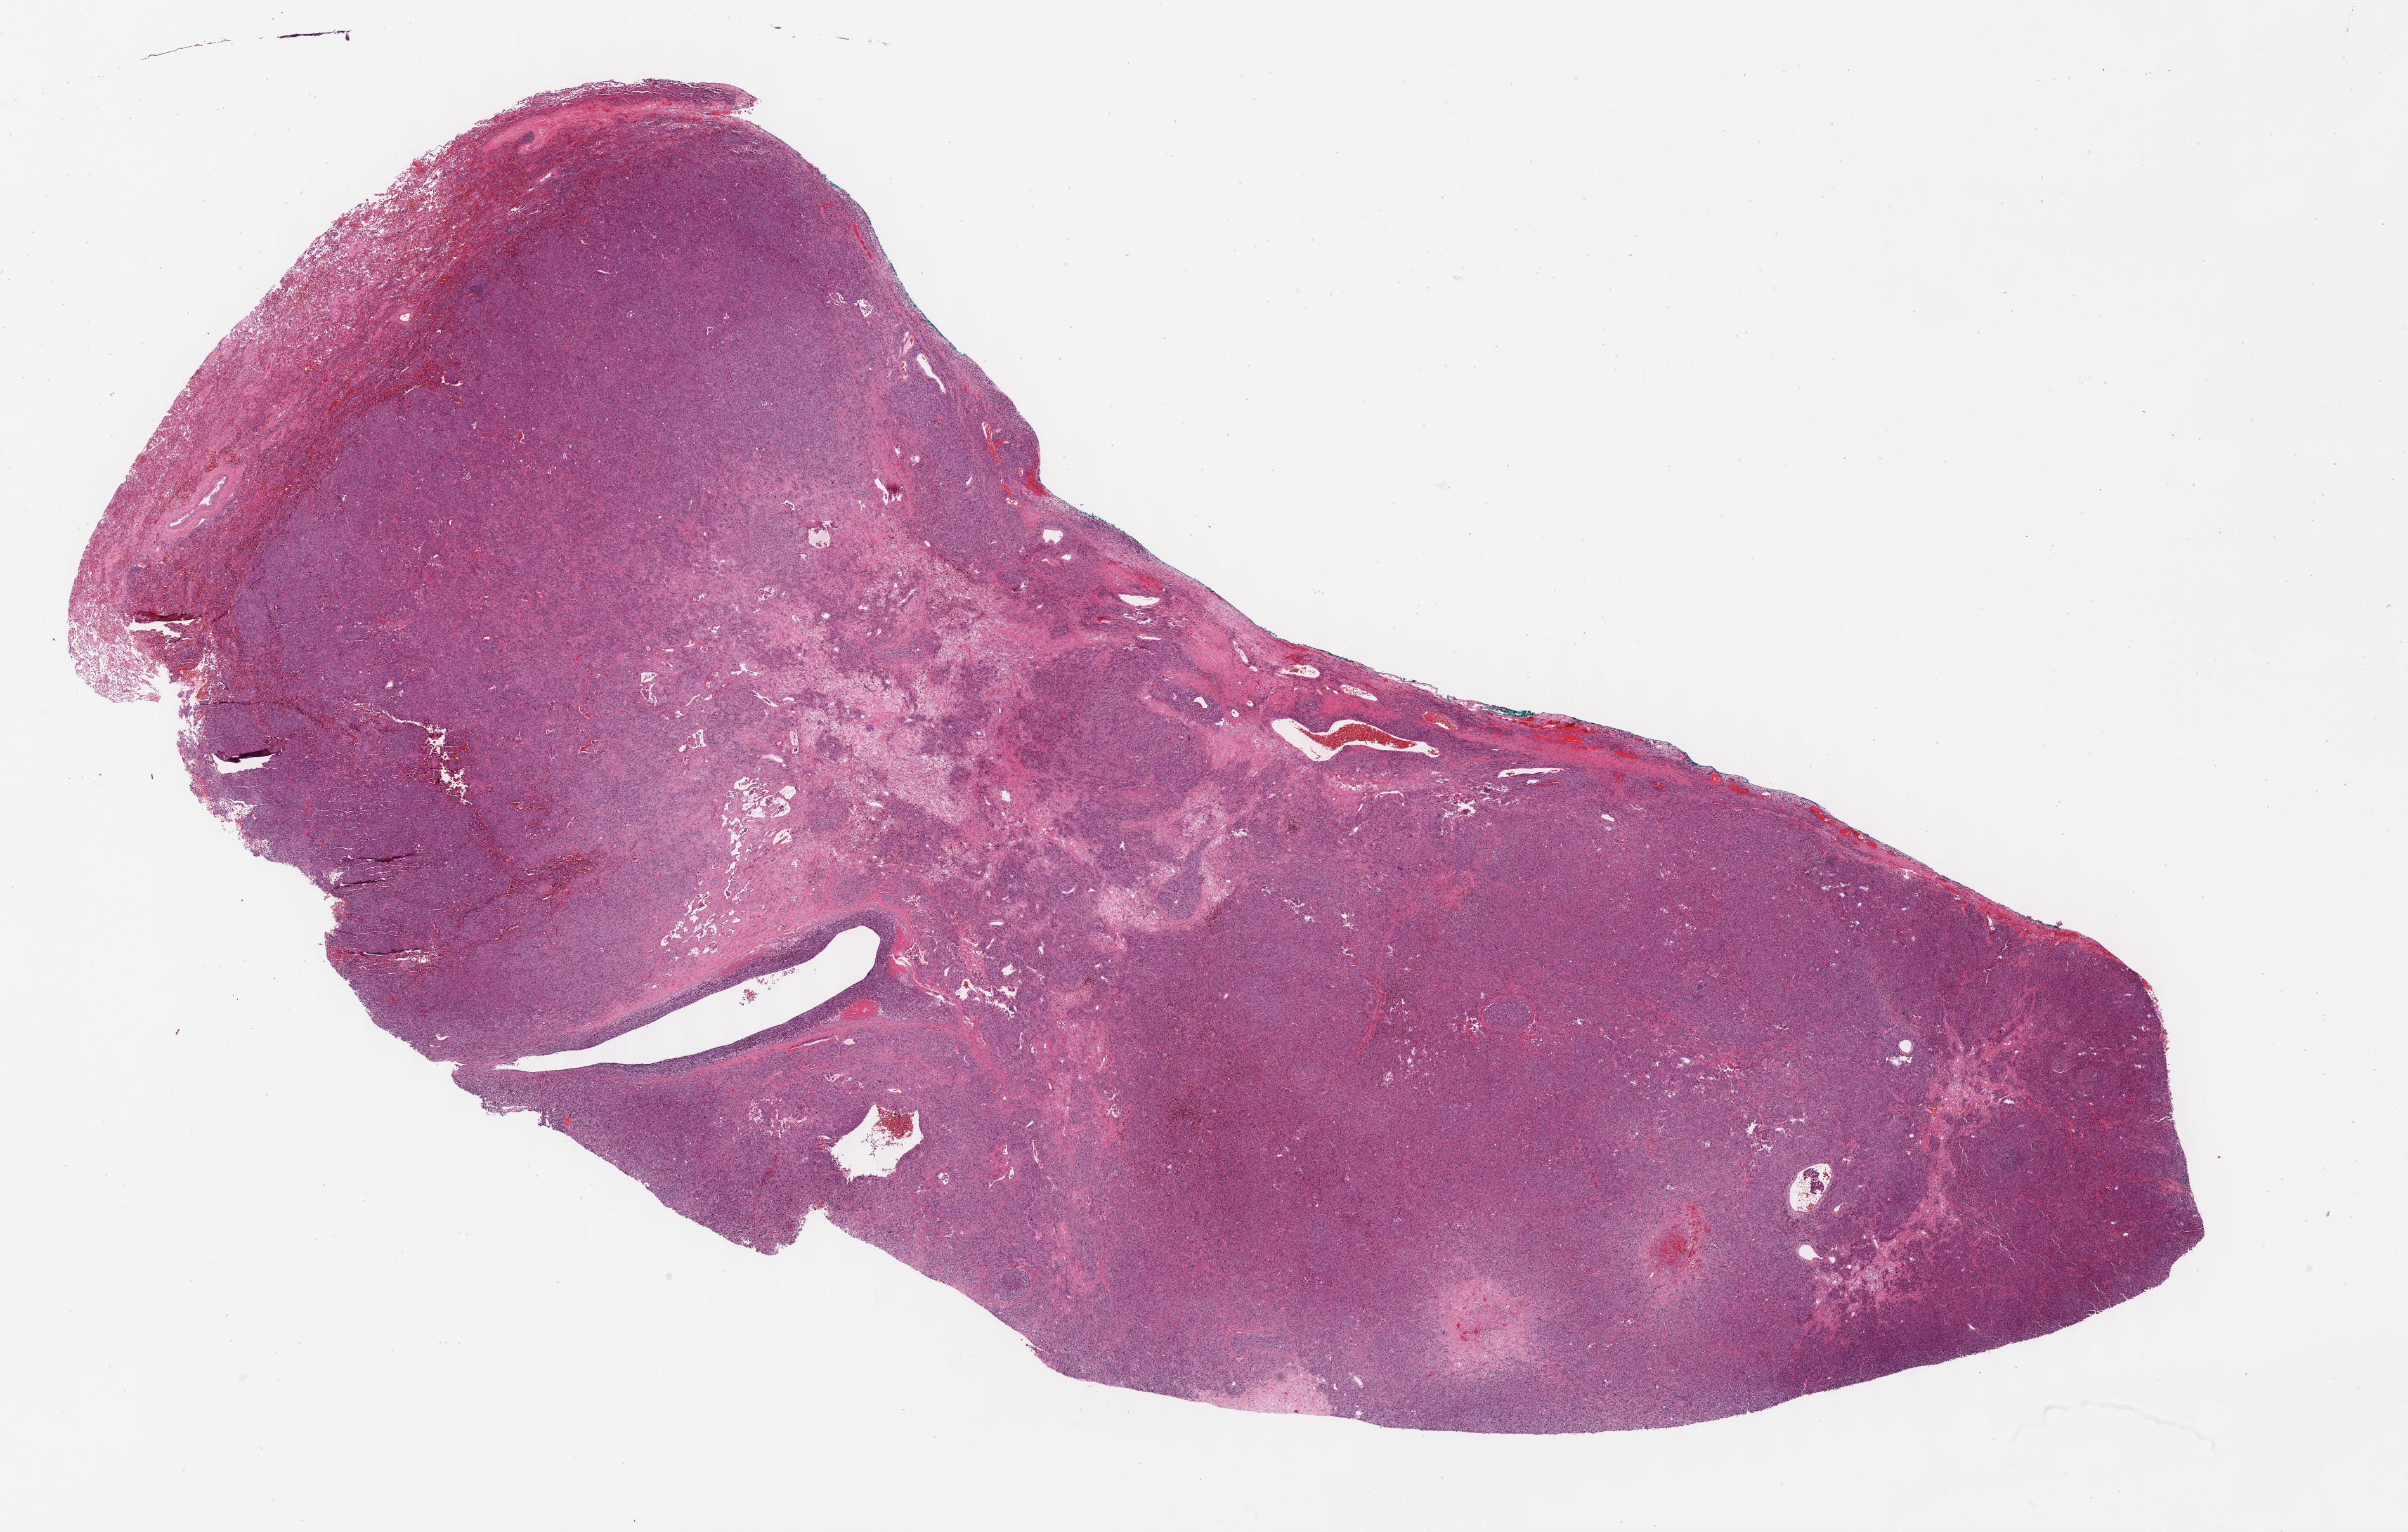
Digitized H&E tissue section (whole slide), low-resolution overview of the scanned area, about 30.7 x 19.5 mm (from a 40x scan). Formalin-fixed paraffin-embedded (FFPE) diagnostic section. Metastatic tumour sample. Male, age 49 years at initial diagnosis.
• this section: metastatic tumour tissue
• patient diagnosis: Malignant melanoma, NOS